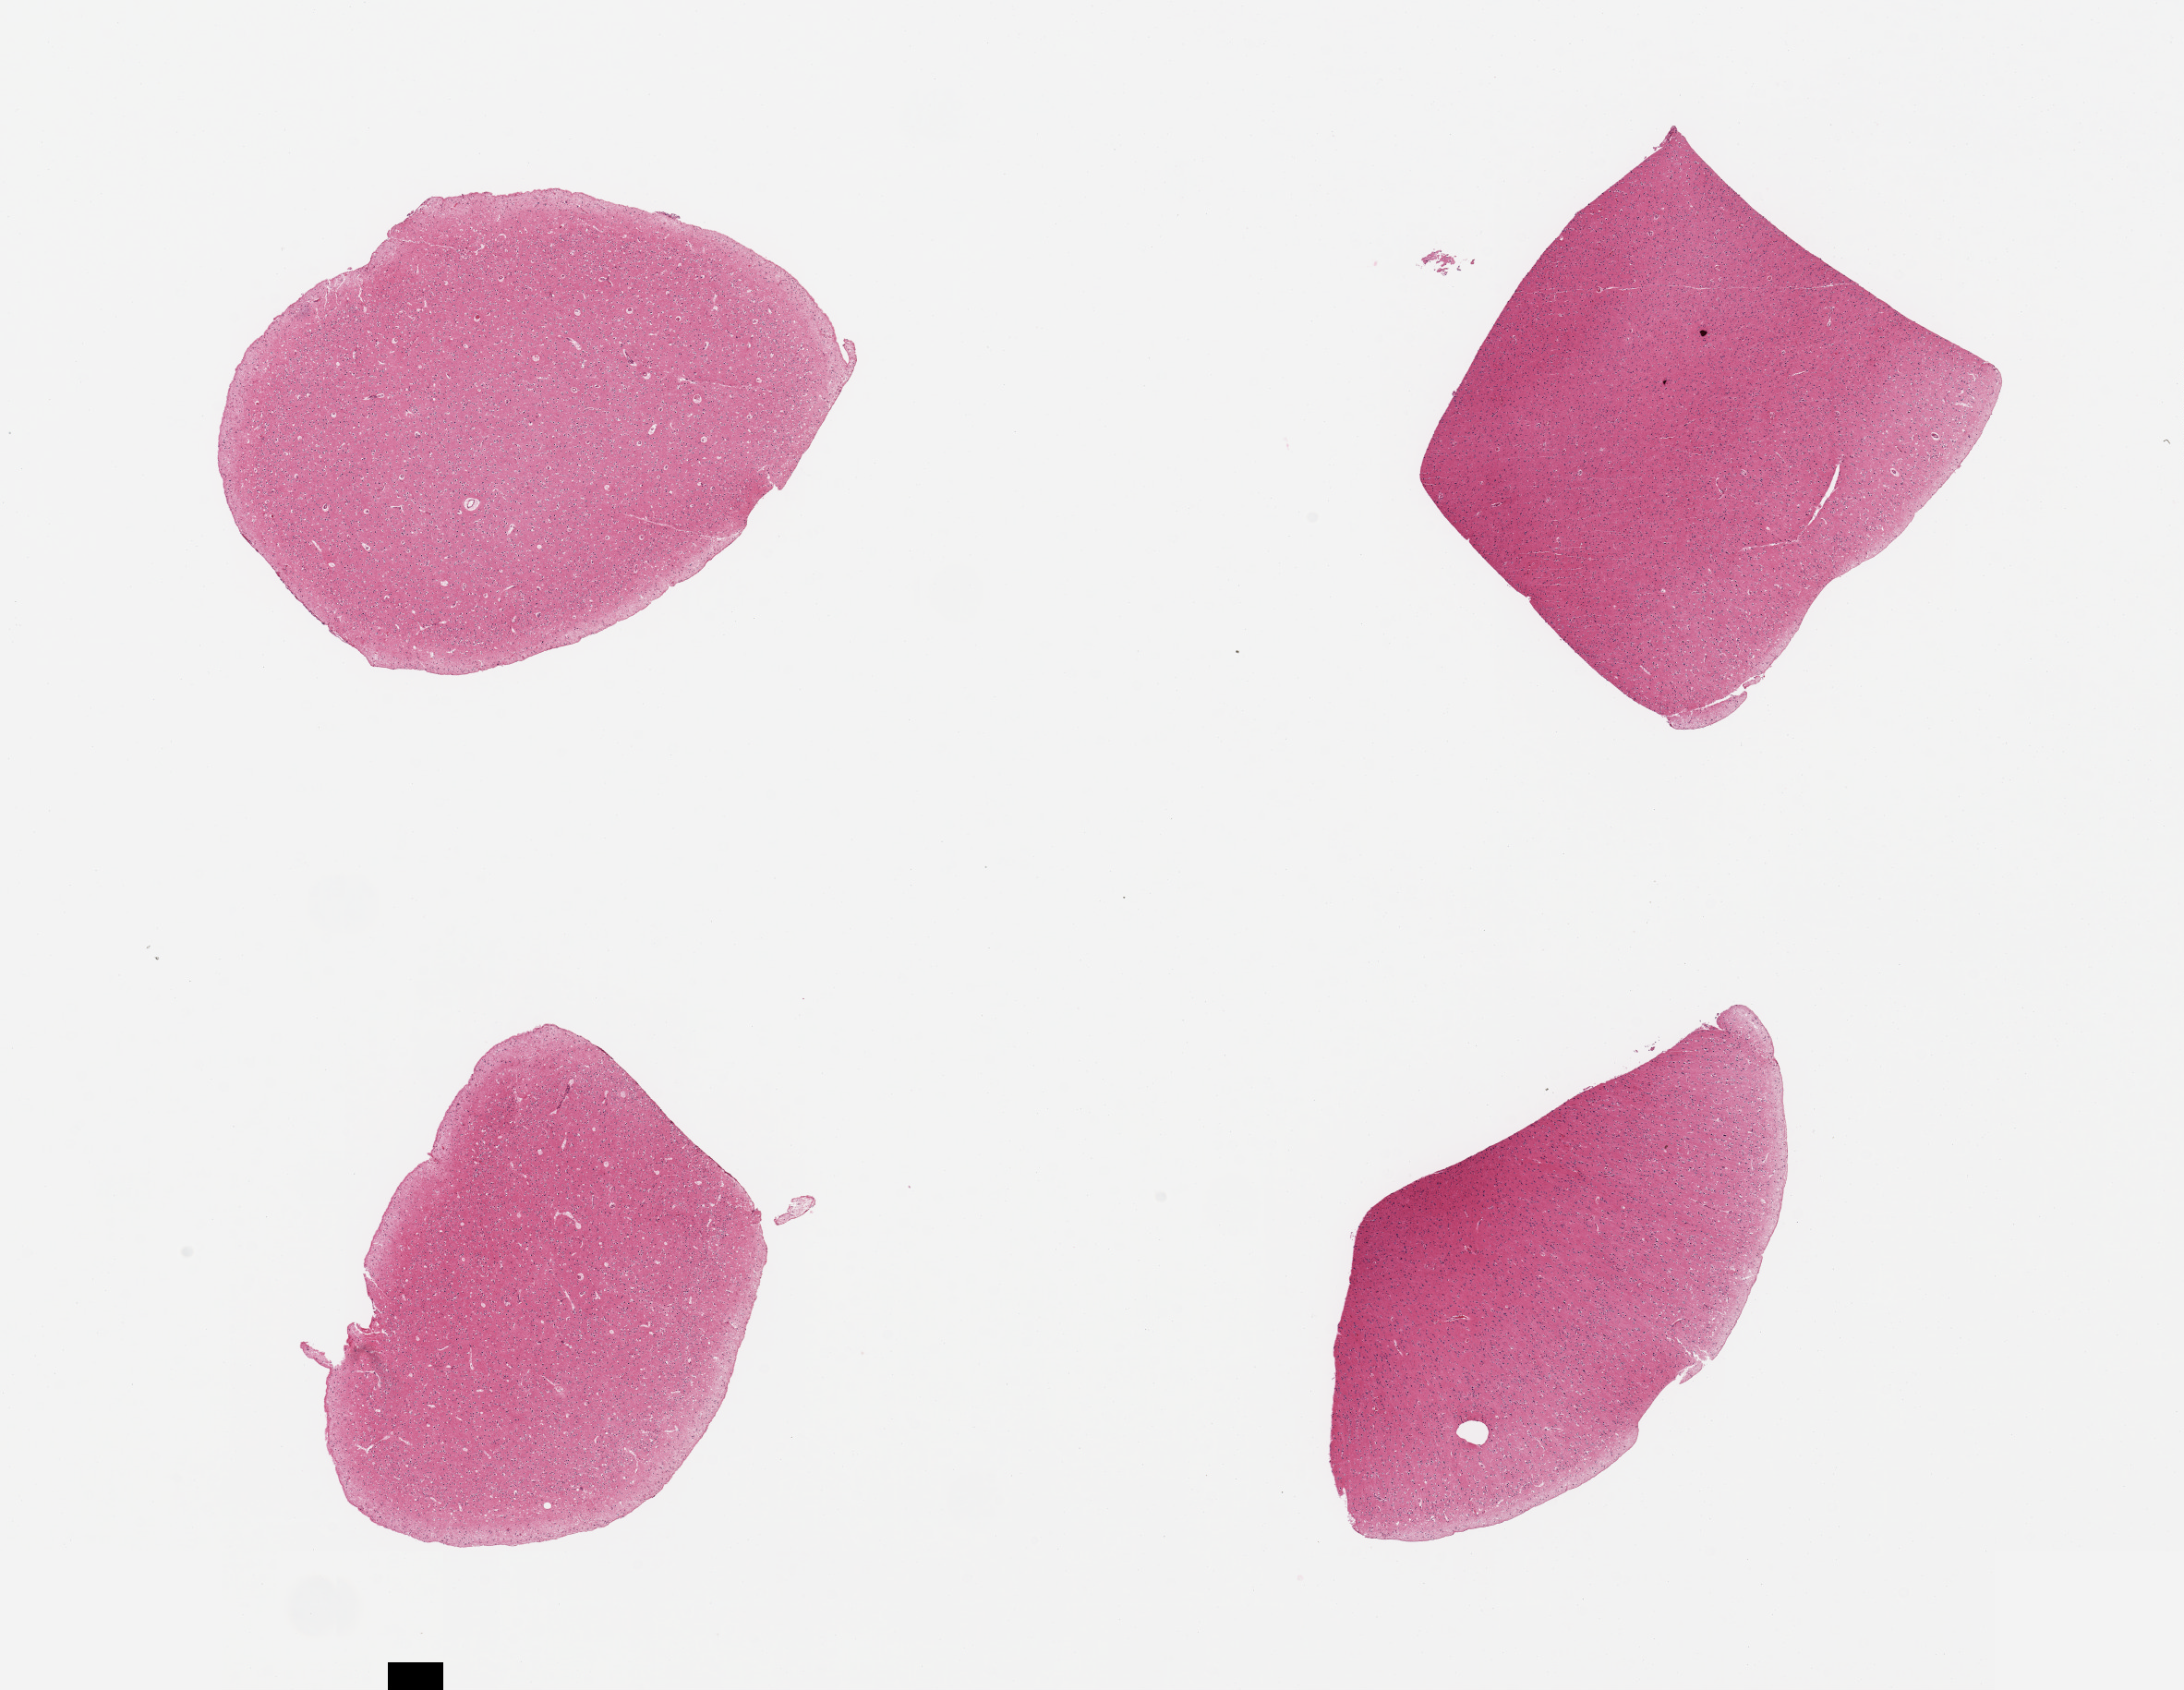
Digitized haematoxylin and eosin-stained section, low-resolution overview of the scanned area, about 18.7 x 14.5 mm, PAXgene-fixed paraffin-embedded (PFPE) section, target tissue: cerebral cortex, tissue donor sample. Male donor.
* pathologist's review note for this sample: 4 pieces, no abnormalities